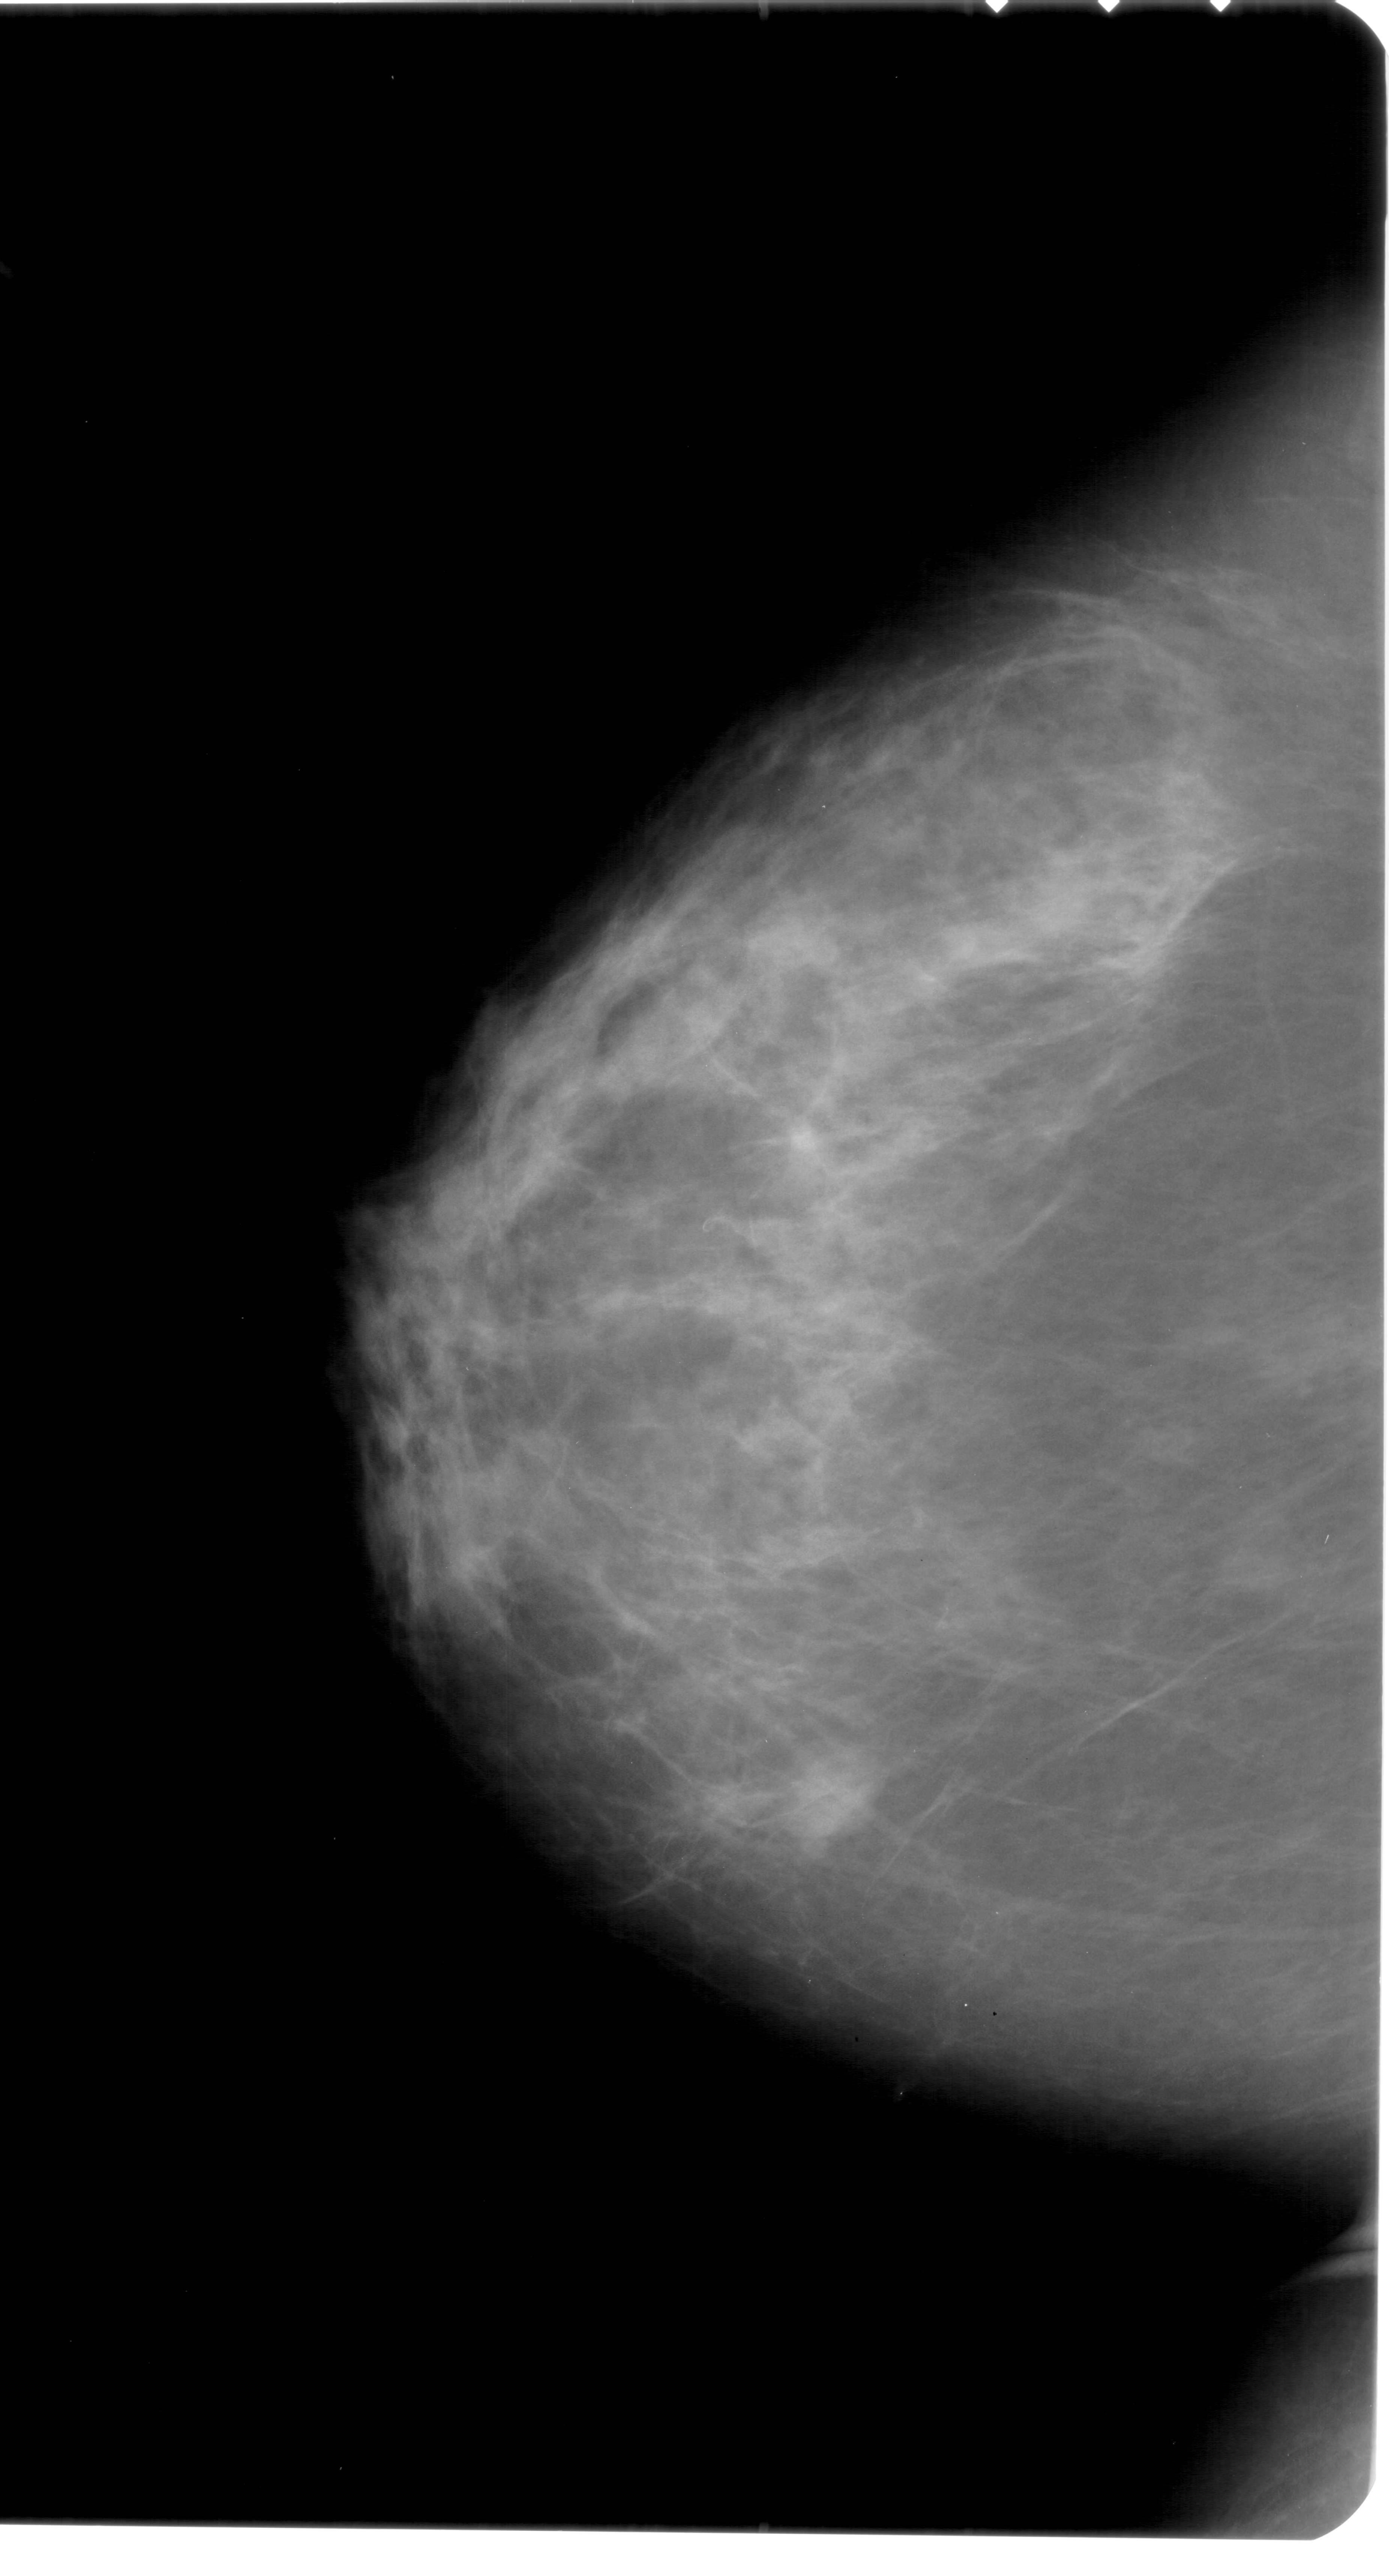
Digitized screen-film mammogram, left breast, CC view, BI-RADS breast density category 3 (scale 1–4).
Mass, shape lobulated, margins obscured; BI-RADS assessment category 4; pathology result (as recorded, not read from the image): benign.